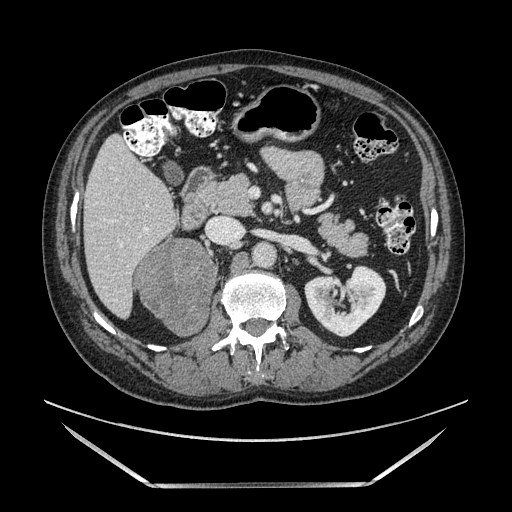
Contrast-enhanced abdominal CT, one axial slice. Position 63 of 185 along the scan axis. Soft-tissue window (W 400 / L 40 HU). 512 × 512 image matrix. Male patient. From the clinical record (not read from this slice): diagnosis: adrenocortical carcinoma; tumour side: right adrenal; tumour size at pathology: 10.3 cm; Ki-67 index: 20 %; stage (as recorded): 3.
Outlined on this slice (semi-automatic segmentation, software-assisted and operator-edited):
- mass: box from (x=138, y=239) to (x=215, y=335) px